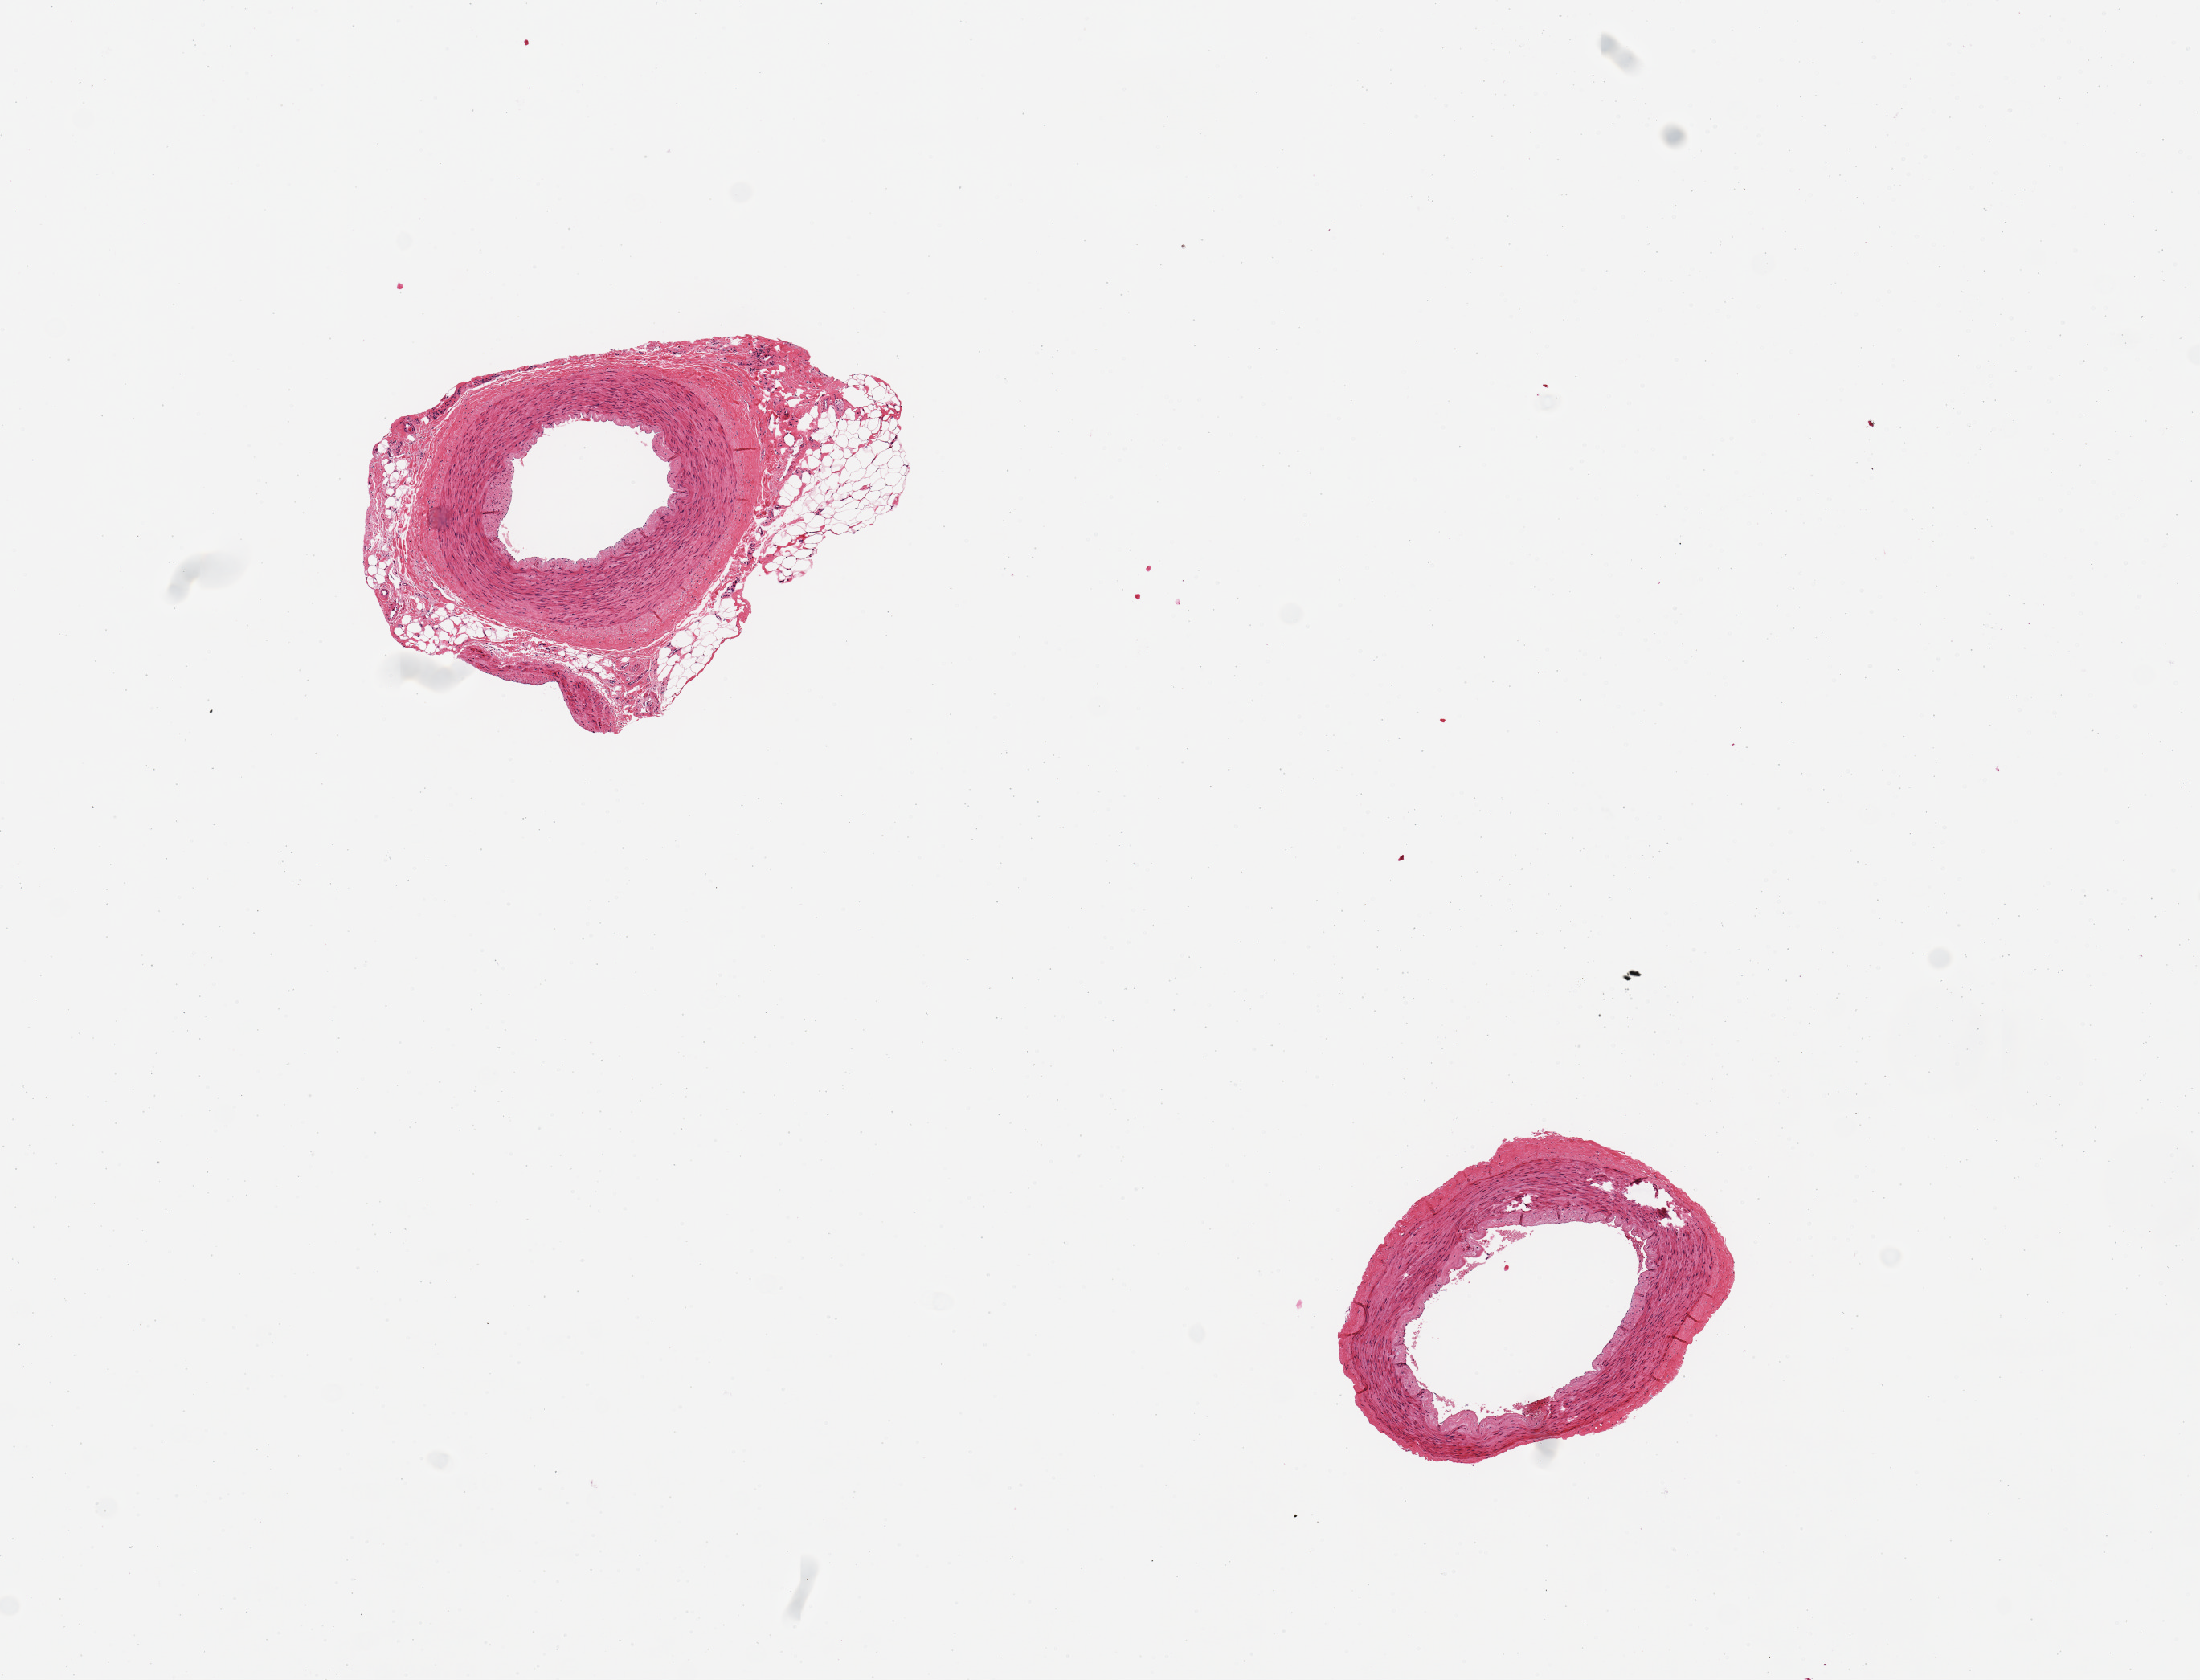
Digitized haematoxylin and eosin-stained section — whole scanned area (about 10.8 x 8.3 mm, slide scanned at 20x) shown as a low-resolution overview, PAXgene-fixed paraffin-embedded (PFPE) section, target tissue: tibial artery, tissue donor sample.
* reviewer comment on this tissue sample: 2 aliquots, ~1.5mm d. One has ~0.5mm nubbins of adherent fat